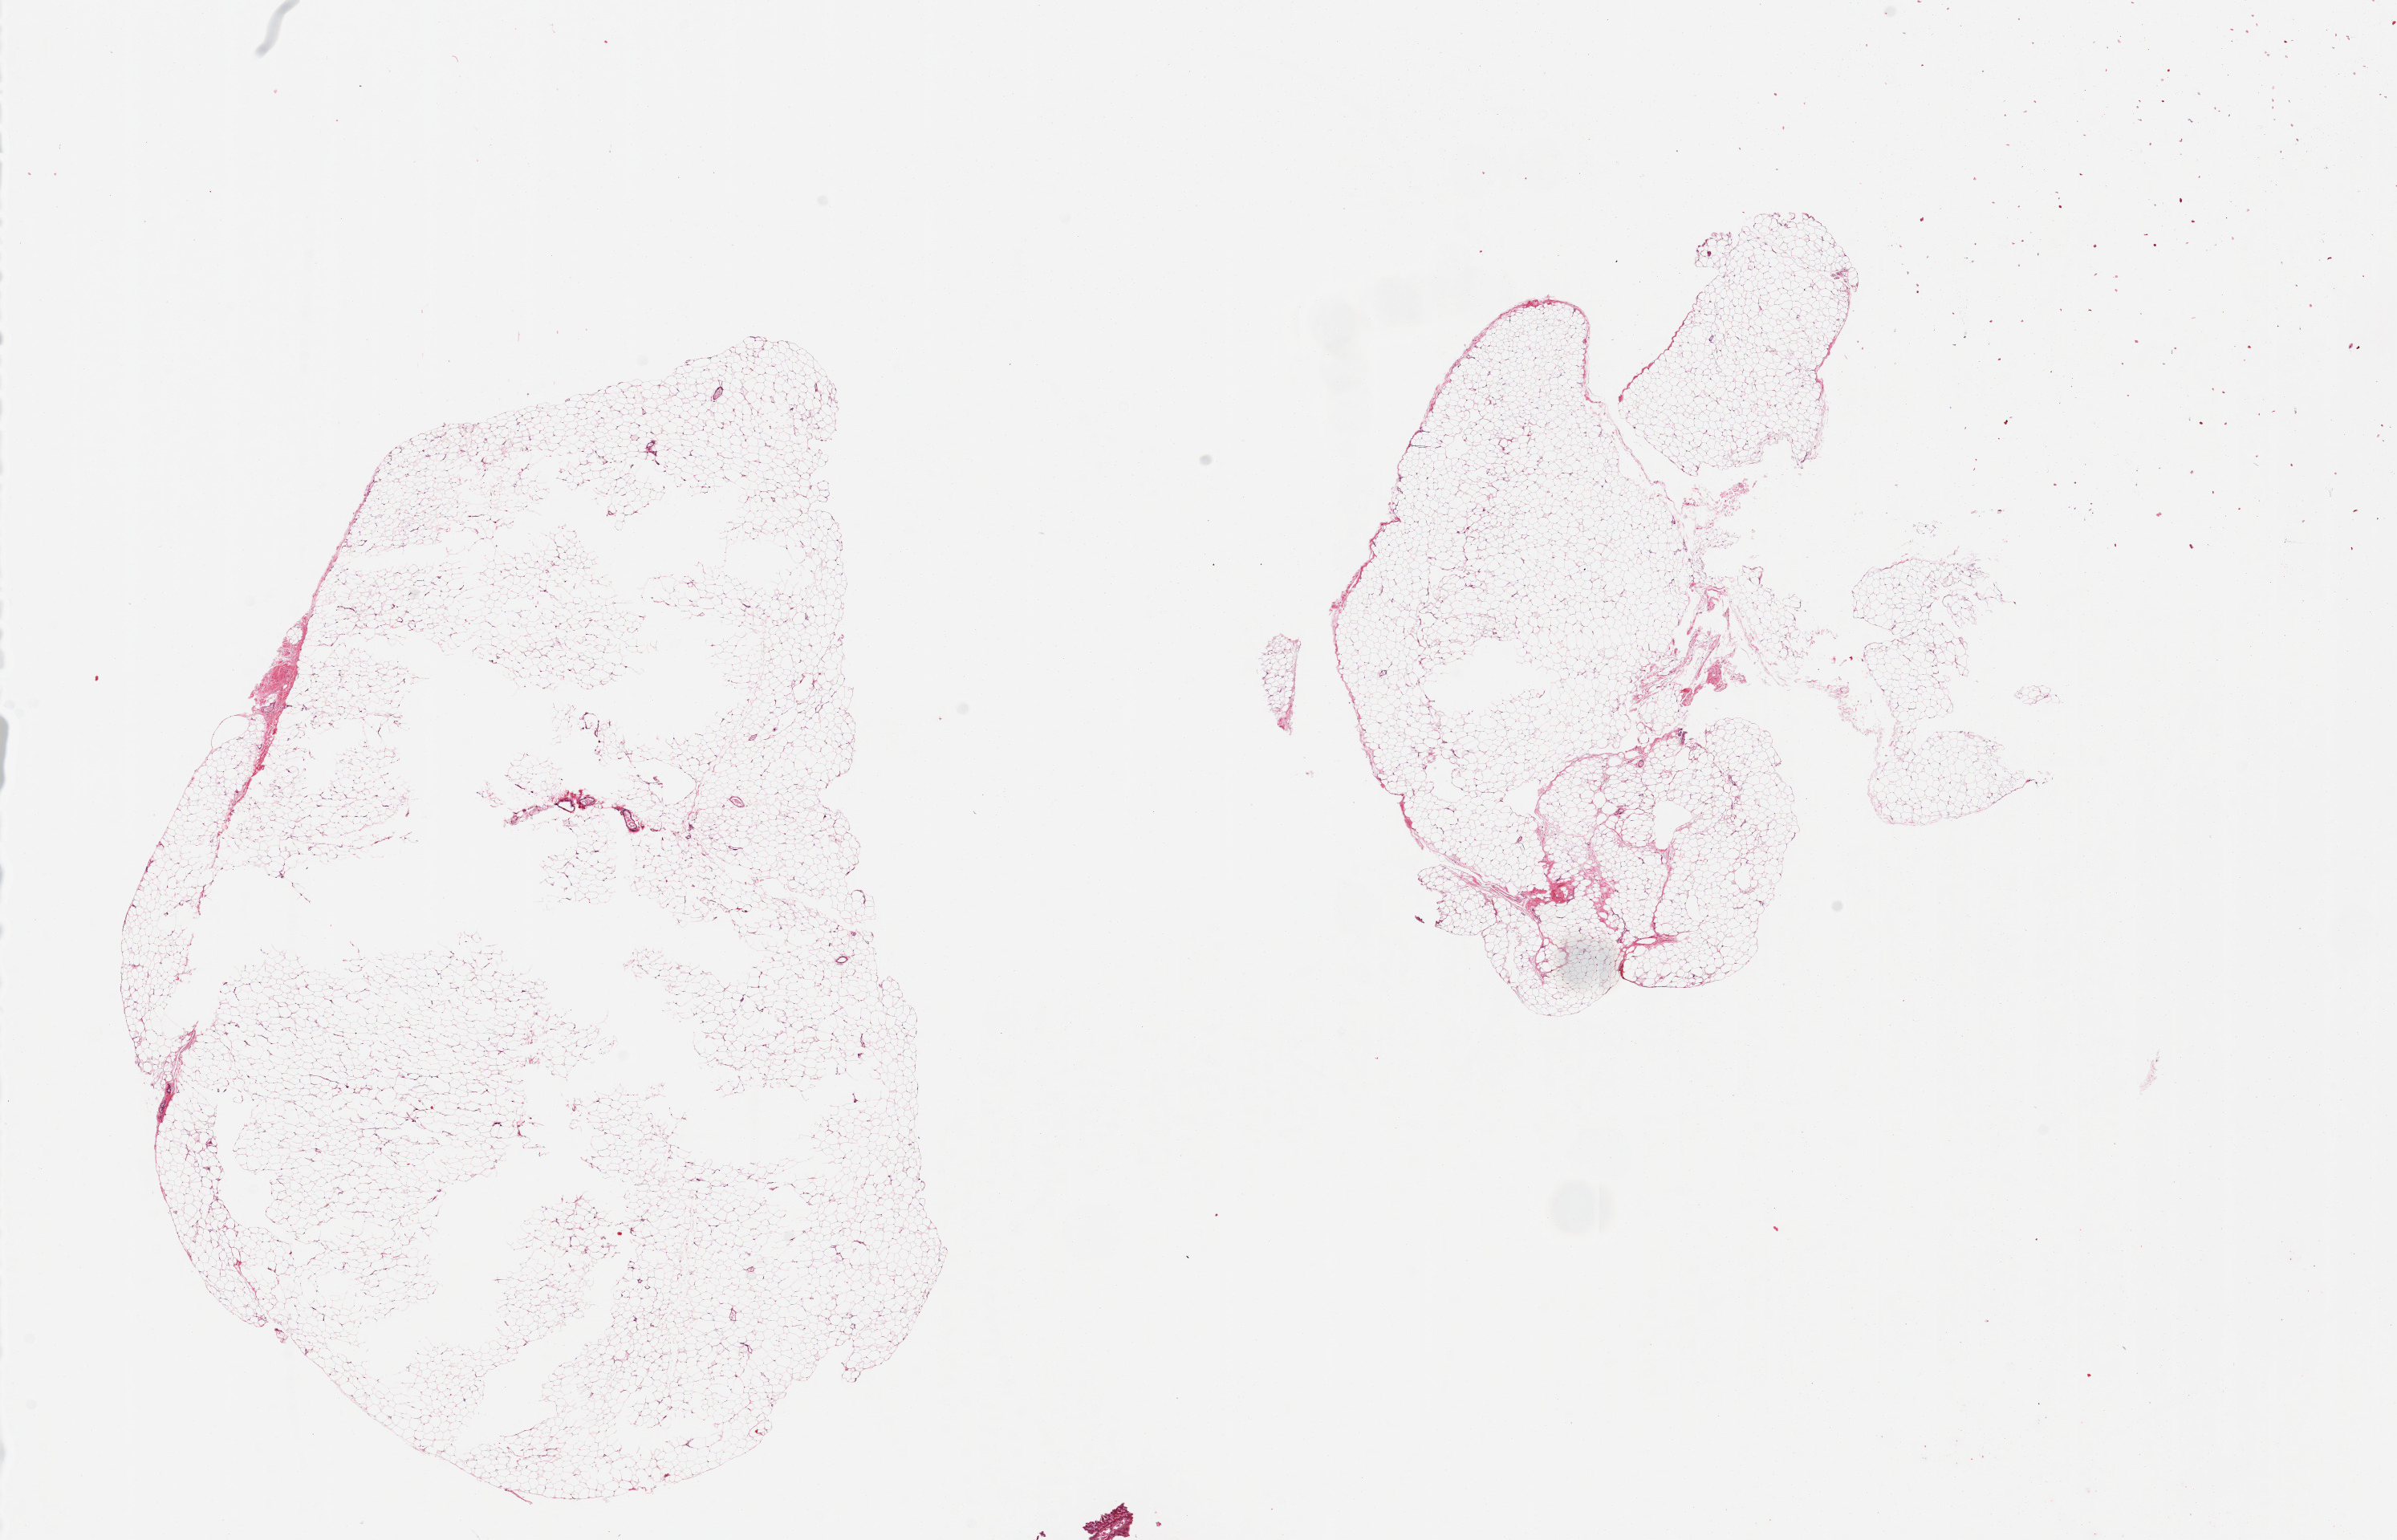
H&E whole-slide image — low-resolution overview of the scanned area, about 23.6 x 15.2 mm (acquisition: 20x scan), PAXgene-fixed paraffin-embedded (PFPE) section, section of adipose tissue (target tissue), tissue donor sample.
Review note (as recorded): 2 pieces, minimal fibrous tissue.